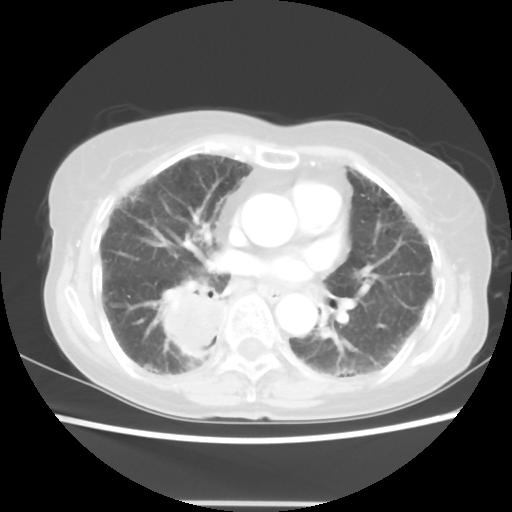
Chest CT, one axial slice. Slice 27 of 52 in the series (ordered by position). Reconstruction kernel STANDARD. 120 kVp. Lung window (W 1500 / L -600 HU). 5 mm slice thickness. 512 × 512 image matrix. Female patient, age 71 years. From the clinical record (not read from this slice): clinical TNM (as recorded): T3 N0 M0.
Annotated regions visible in this slice (bounding box drawn by a radiologist):
- lung tumour (recorded histology: squamous cell carcinoma): box from (x=146, y=282) to (x=239, y=364) px